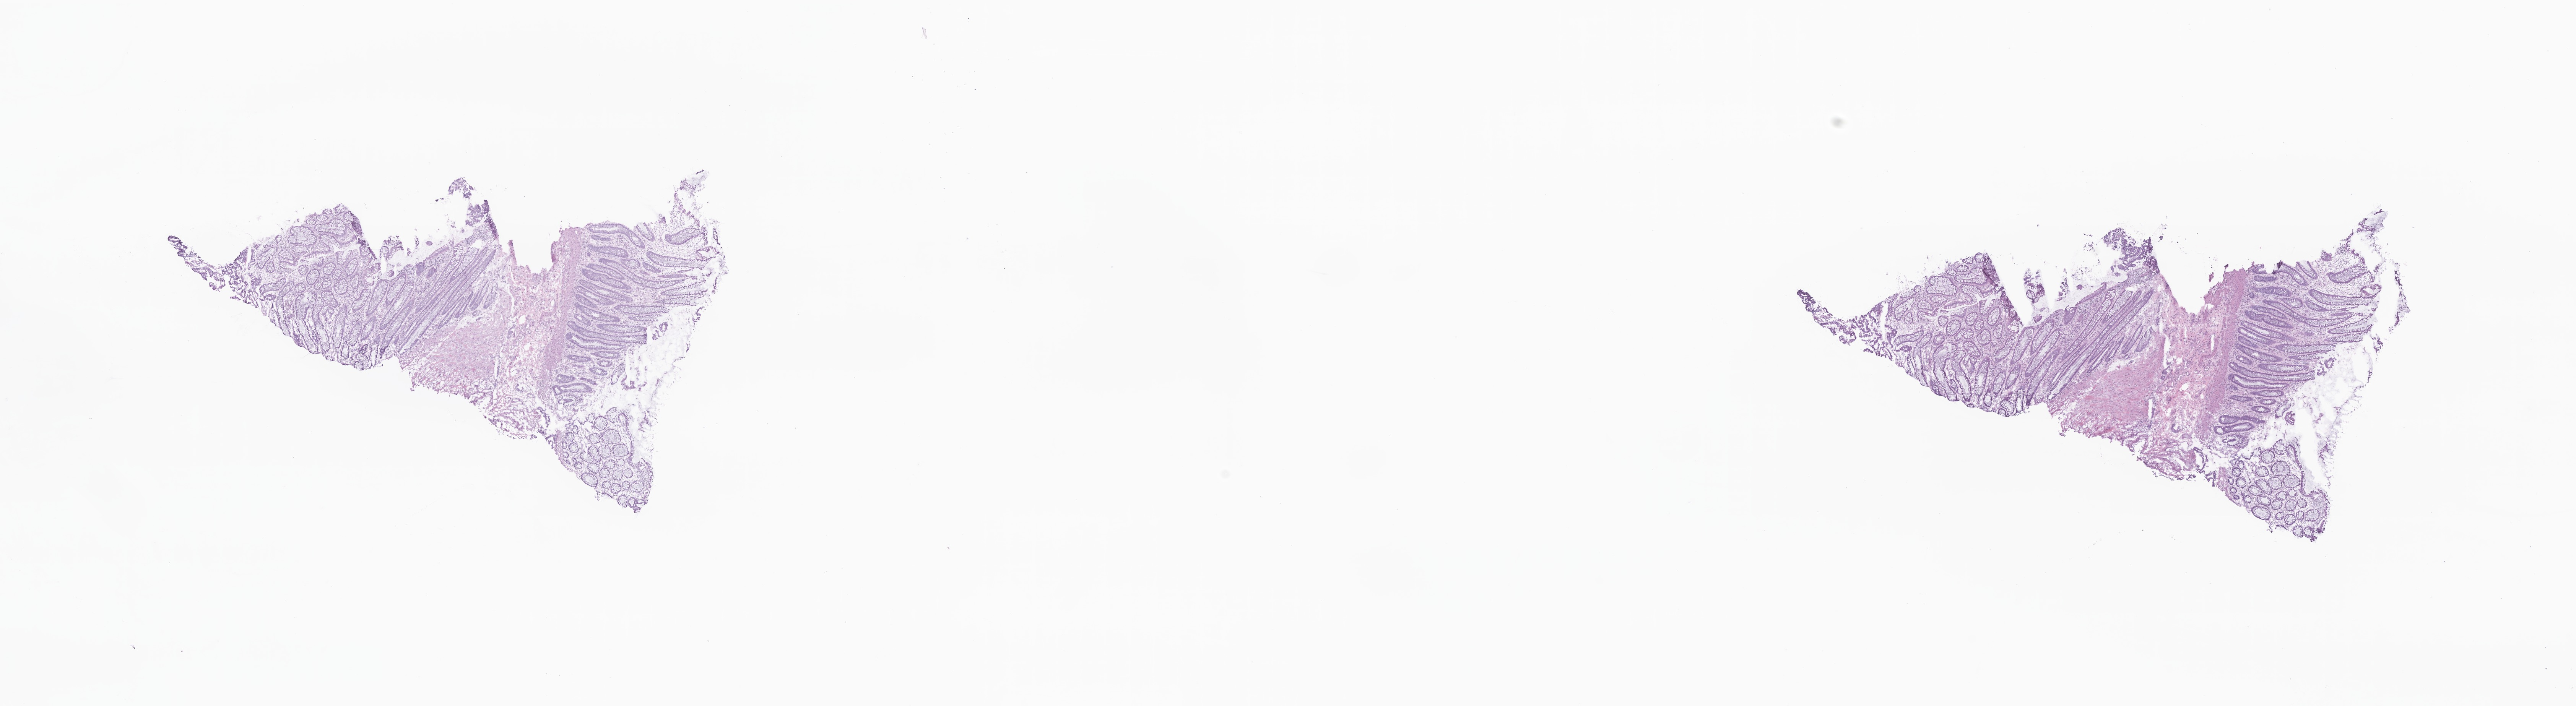
Whole-slide image, H&E stain, shown as a low-resolution overview of the whole scanned area (about 28.4 x 7.8 mm); frozen section (tissue freezing medium); specimen: primary tumor; site: sigmoid colon. Patient: male, age at initial diagnosis 60 years. Pathologist review of this section (percent, as recorded): tumor cells 12%, tumor nuclei 35%, stromal cells 32%, necrosis 1%, normal cells 55%. Inflammatory infiltration, as recorded: lymphocyte infiltration 18%, monocyte infiltration 1%, neutrophil infiltration 0%.
Section: top of the tissue portion. Histologic diagnosis: Adenocarcinoma, NOS.